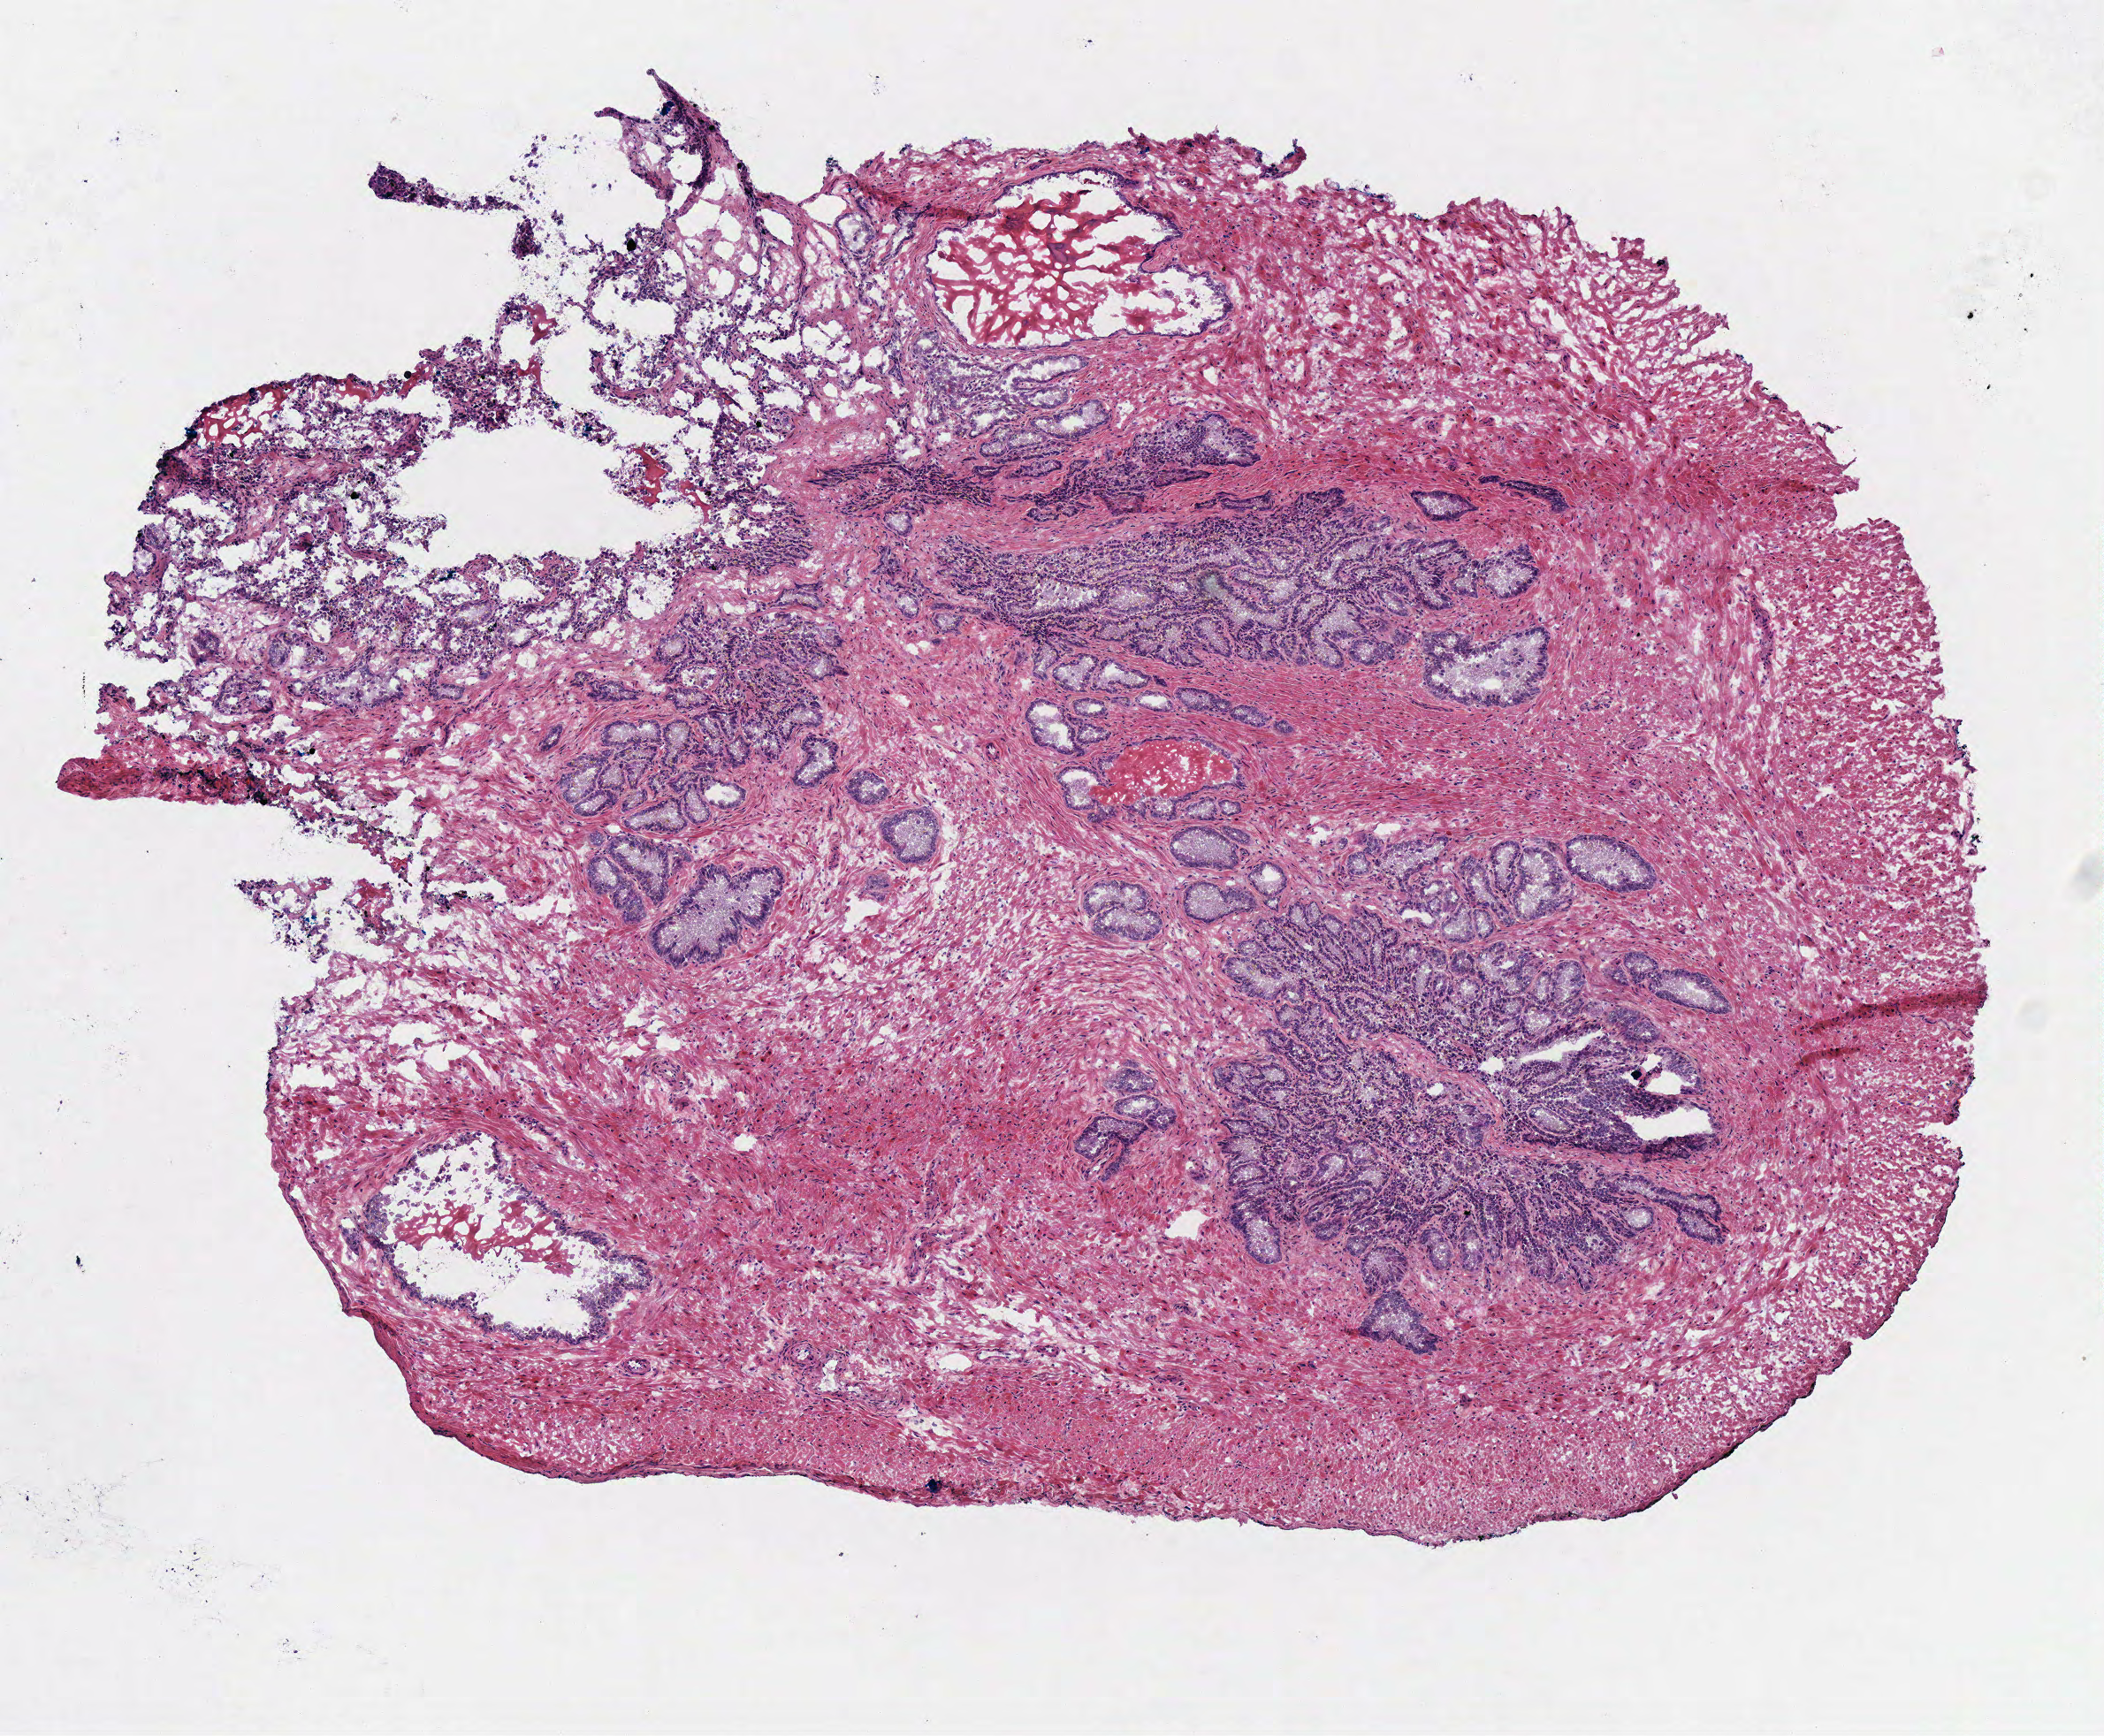
Whole-slide histology image, H&E, a low-resolution overview of the entire scanned area, about 4.7 x 3.9 mm, frozen section, prostate, solid tissue normal (non-tumour tissue) sample. Male patient; age at initial diagnosis 62 years.
This section: solid tissue normal (non-tumour) sample from the same patient. Patient diagnosis: Acinar cell carcinoma (prostate gland).